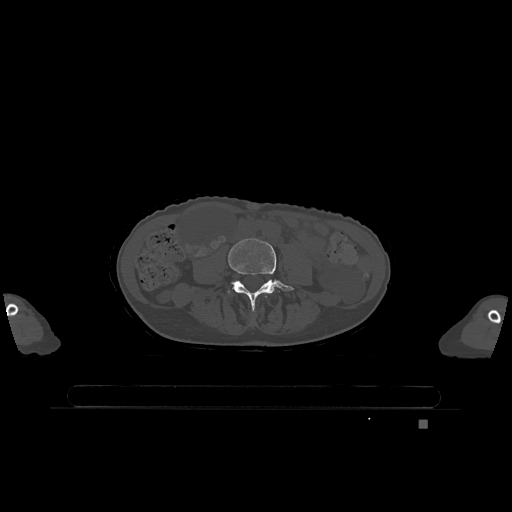
CT including the spine, one axial slice; slice 296 of 1317 in the series (ordered by position); bone window (W 1800 / L 400 HU); 0.5 mm slice thickness; 512 × 512 image matrix, field of view 500 × 500 mm. Patient: female, 74 years. Case-level facts recorded for this patient, not image findings: primary cancer: lung; vertebrae with lytic lesions (as recorded): T1, T4, T5, T6, L4, L5.
Annotated regions visible in this slice (semi-automatically segmented with operator editing):
- L3 vertebra: bounding box [x1, y1, x2, y2] px = [265, 296, 267, 298]
- L4 vertebra: [228, 238, 294, 310]